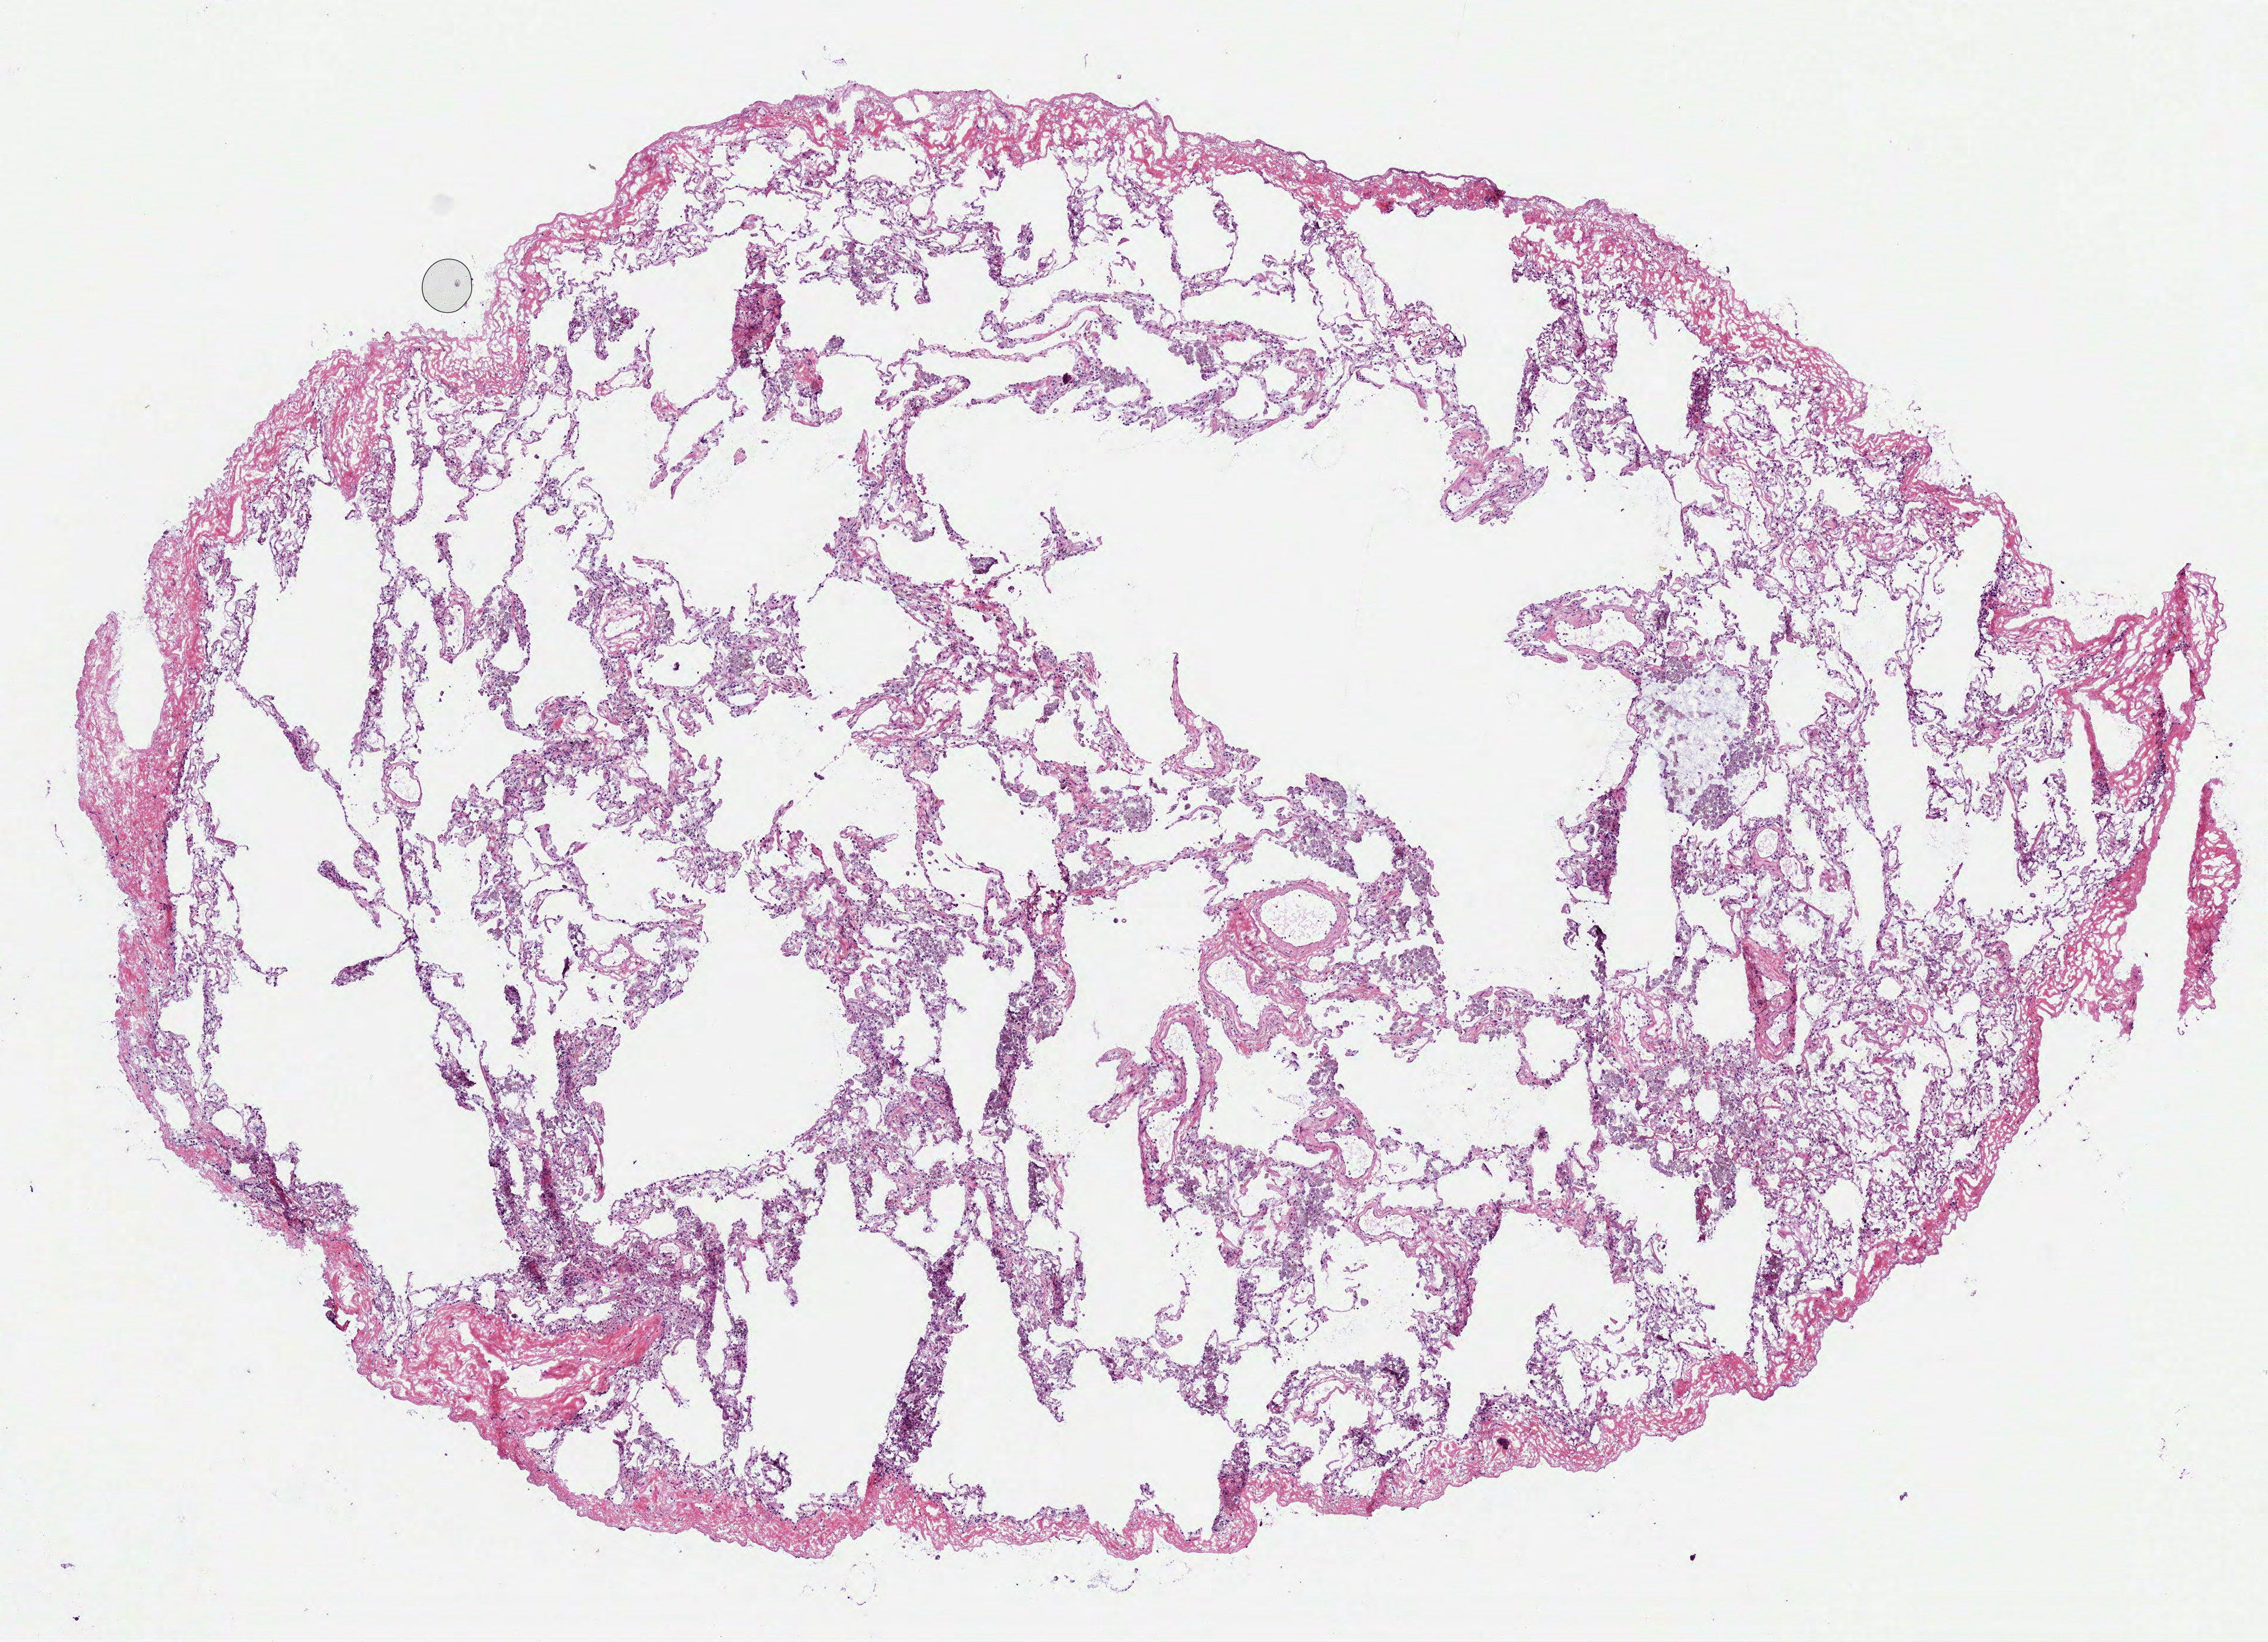
Digitized Hematoxylin and eosin (H&E) stained tissue section (whole slide), a low-resolution overview of the entire scanned area, about 7.7 x 5.6 mm. Frozen section. Solid tissue normal (non-tumour tissue) sample from the lung. Female, age 76 years at initial diagnosis.
* this section: solid tissue normal sample (biorepository sample class)
* patient diagnosis: Adenocarcinoma, NOS